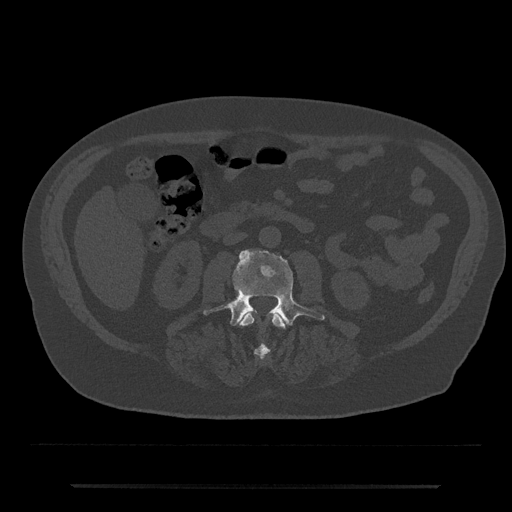
CT including the spine, one axial slice. Slice 427 of 797 in the series (ordered by position). Reconstruction kernel Br40s/3. 120 kVp. Bone window (W 1800 / L 400 HU). 0.5 mm slice thickness. 512 × 512 image matrix, field of view 434 × 434 mm. Male patient, age 80 years. From the clinical record (not read from this slice): primary cancer: prostate.
Structures marked on this image (semi-automatic segmentation, software-assisted and operator-edited):
- L2 vertebra: bounding box <240,311,285,358> (left, top, right, bottom; pixels)
- L3 vertebra: <203,250,325,326>